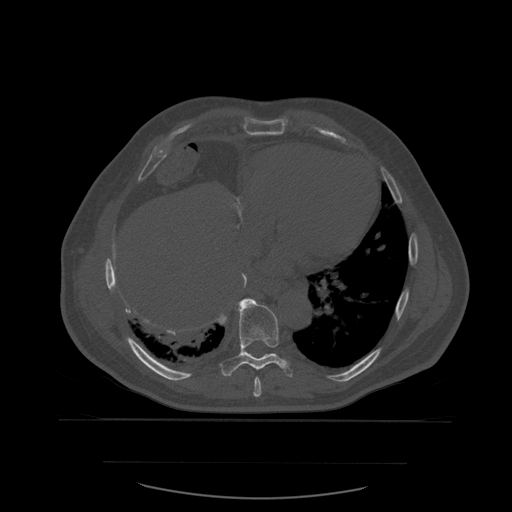
CT including the spine, one axial slice. Position 341 of 590 along the scan axis. Bone window (W 1800 / L 400 HU). 1.25 mm slice thickness. 512 × 512 image matrix, field of view 479 × 479 mm. Patient age 71 years. From the clinical record (not read from this slice): primary cancer: lung.
Annotated regions visible in this slice (semi-automatic segmentation, software-assisted and operator-edited):
- T8 vertebra: bounding box <254,377,262,397> (left, top, right, bottom; pixels)
- T9 vertebra: <220,298,293,378>